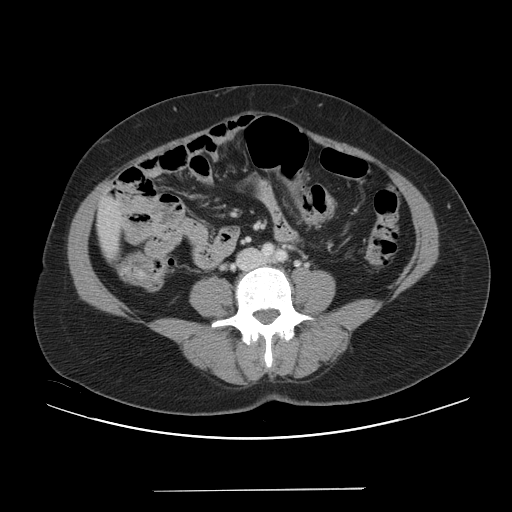
Contrast-enhanced abdominal CT, one axial slice; slice 4 of 56 in the series (ordered by position); 120 kVp; intravenous contrast given; soft-tissue window (W 400 / L 40 HU); 5 mm slice thickness; 512 × 512 image matrix, field of view 419 × 419 mm. Female patient, age 54 years. From the clinical record (not read from this slice): diagnosis: colorectal cancer liver metastases, imaged before liver resection; multiple liver metastases: yes; largest metastasis: 3.2 cm; disease in both lobes: yes.
Annotated regions visible in this slice (expert manual segmentation):
- liver: bounding box [x1, y1, x2, y2] px = [98, 196, 122, 258]